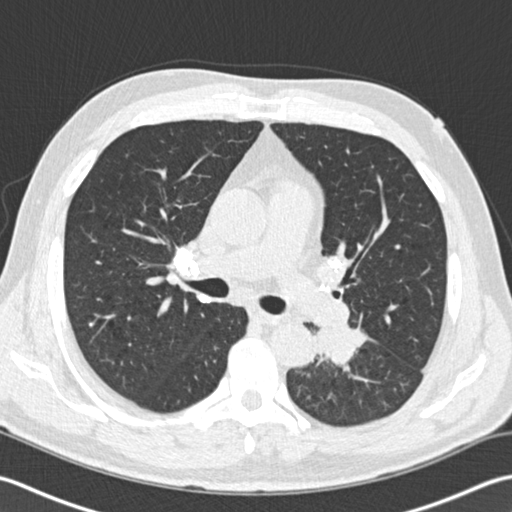
Low-dose screening chest CT, one axial slice. 120 kVp. Lung window (W 1500 / L -600 HU). 512 × 512 image matrix, field of view 350 × 350 mm.
Structures marked on this image (expert manual segmentation):
- lesion 1 (tumor, lower lobe of left lung): bounding box <316,321,368,367> (left, top, right, bottom; pixels)